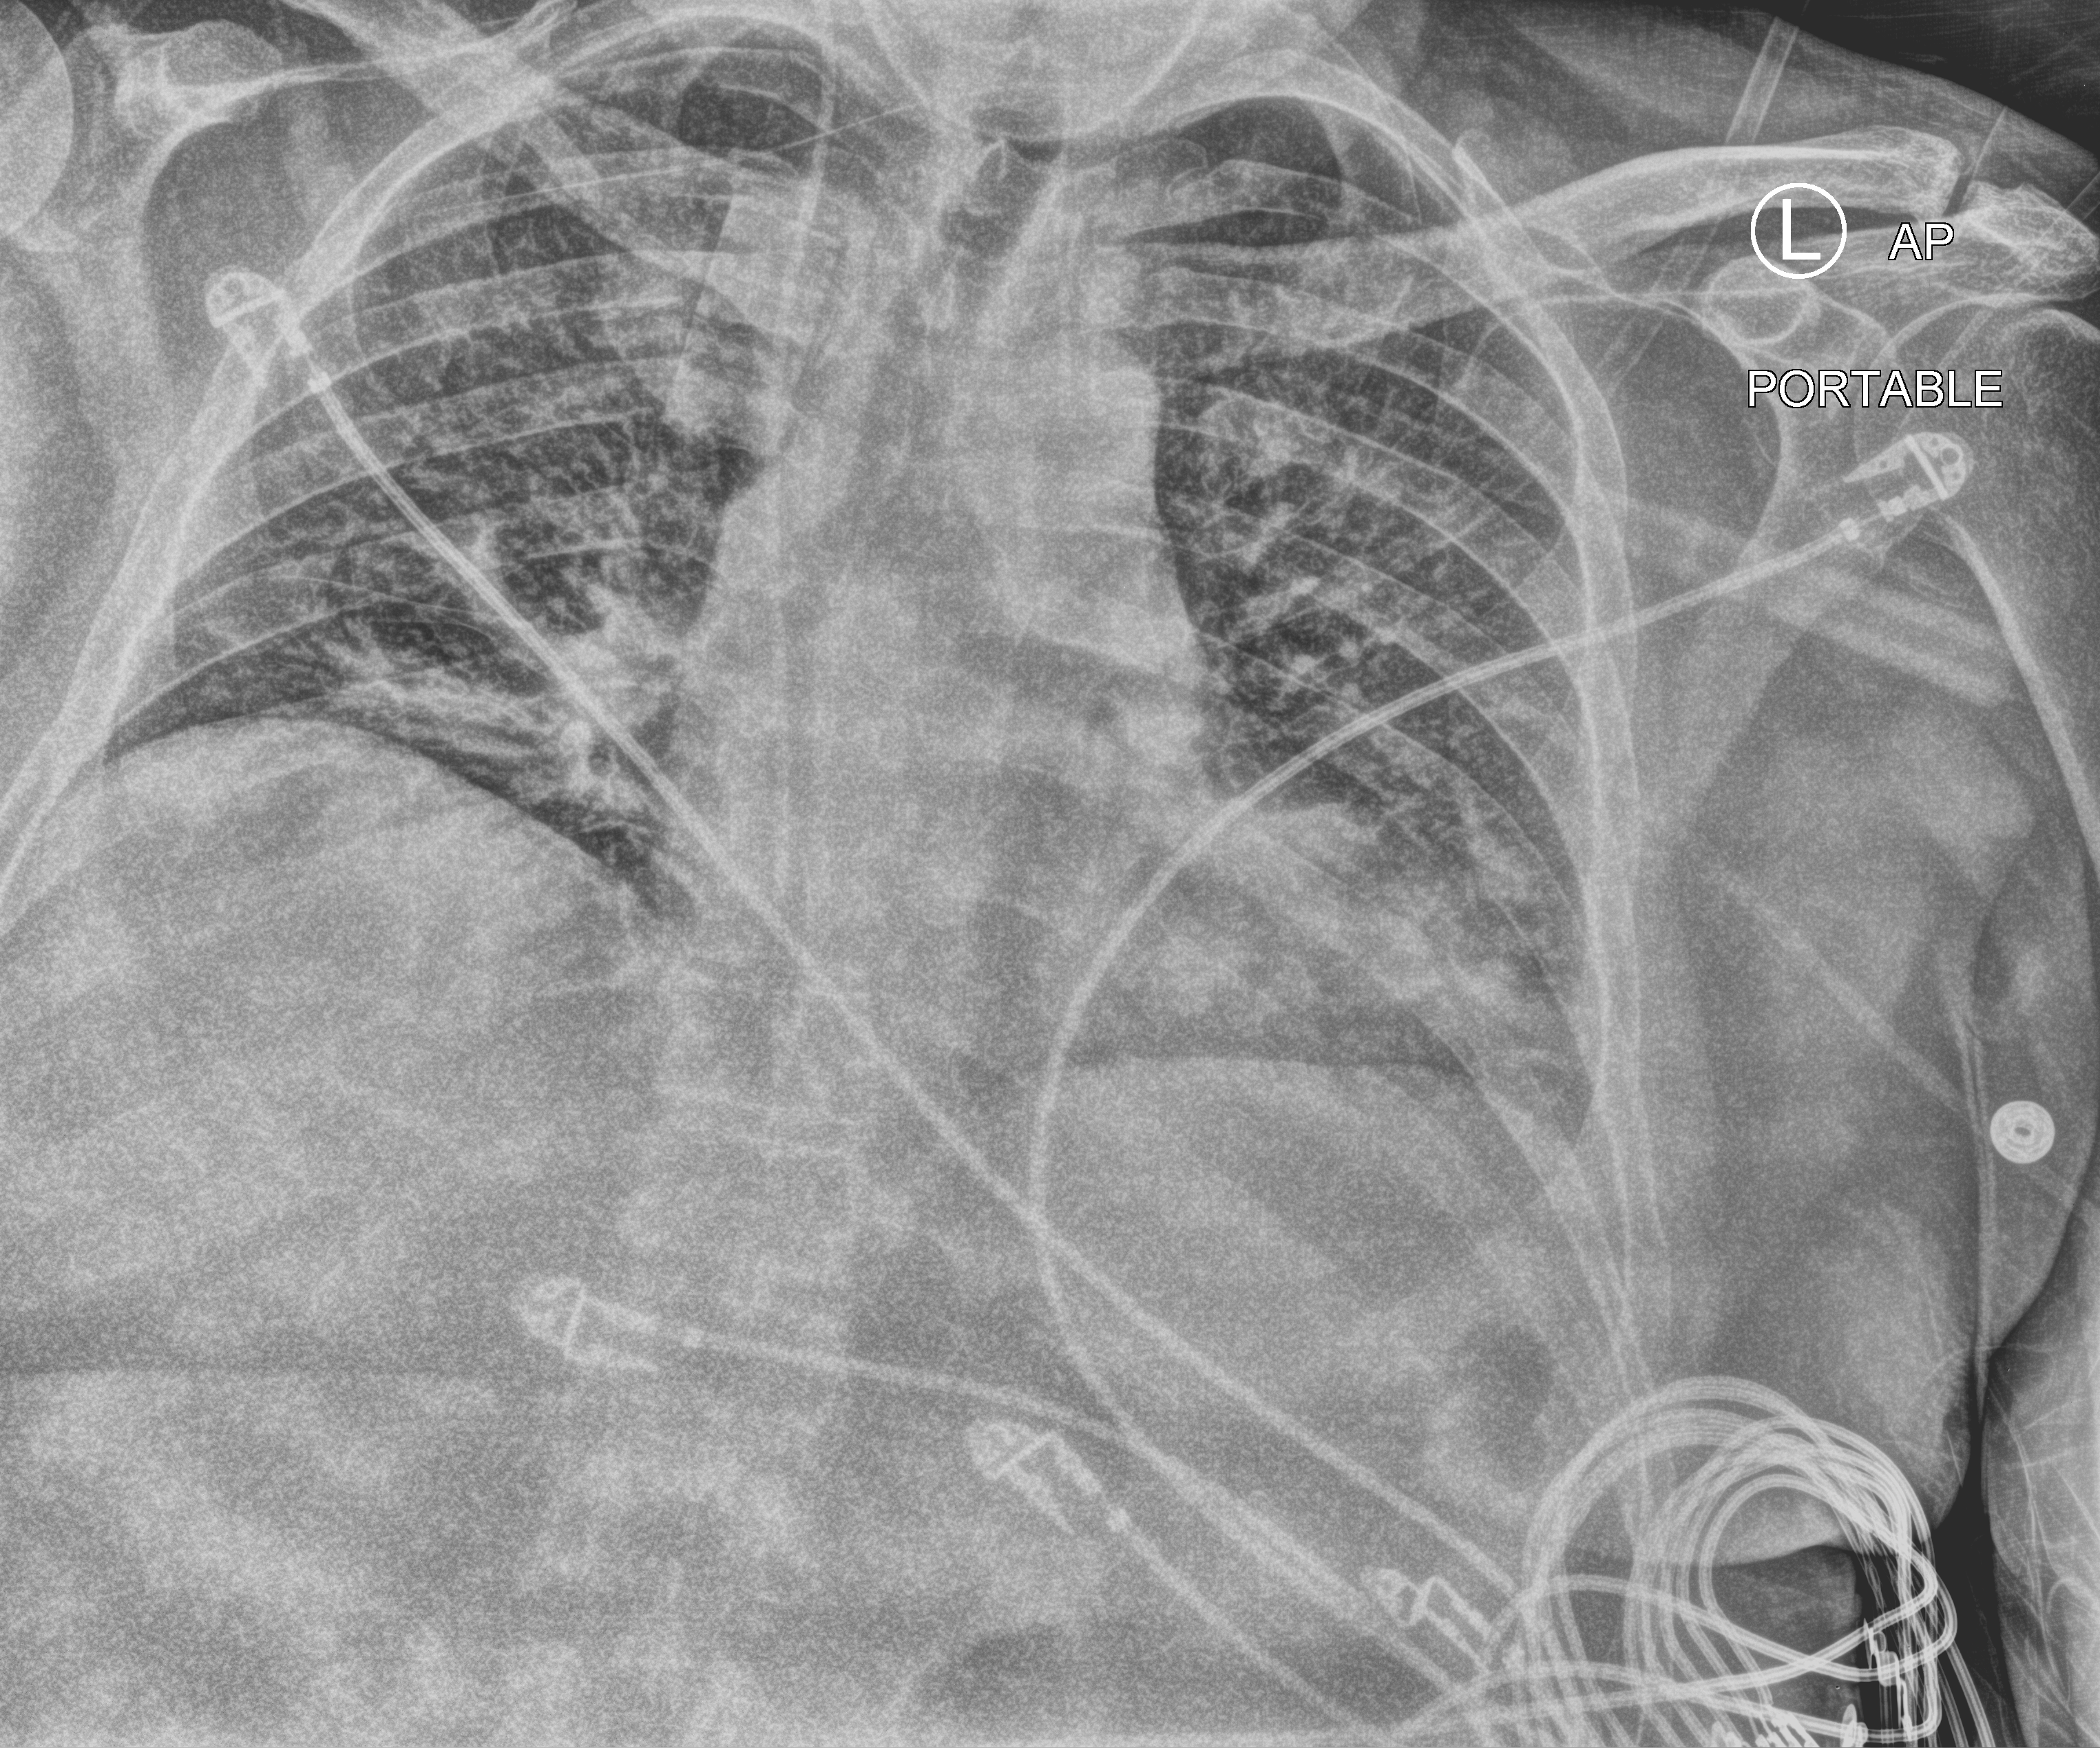
Chest X-ray (portable), anteroposterior (AP) projection. Patient hospitalised with COVID-19; male, aged 18–59 years.
Admission-level facts for this patient (not findings on this image; timing relative to this image not recorded): mechanically ventilated during this hospital stay: yes.